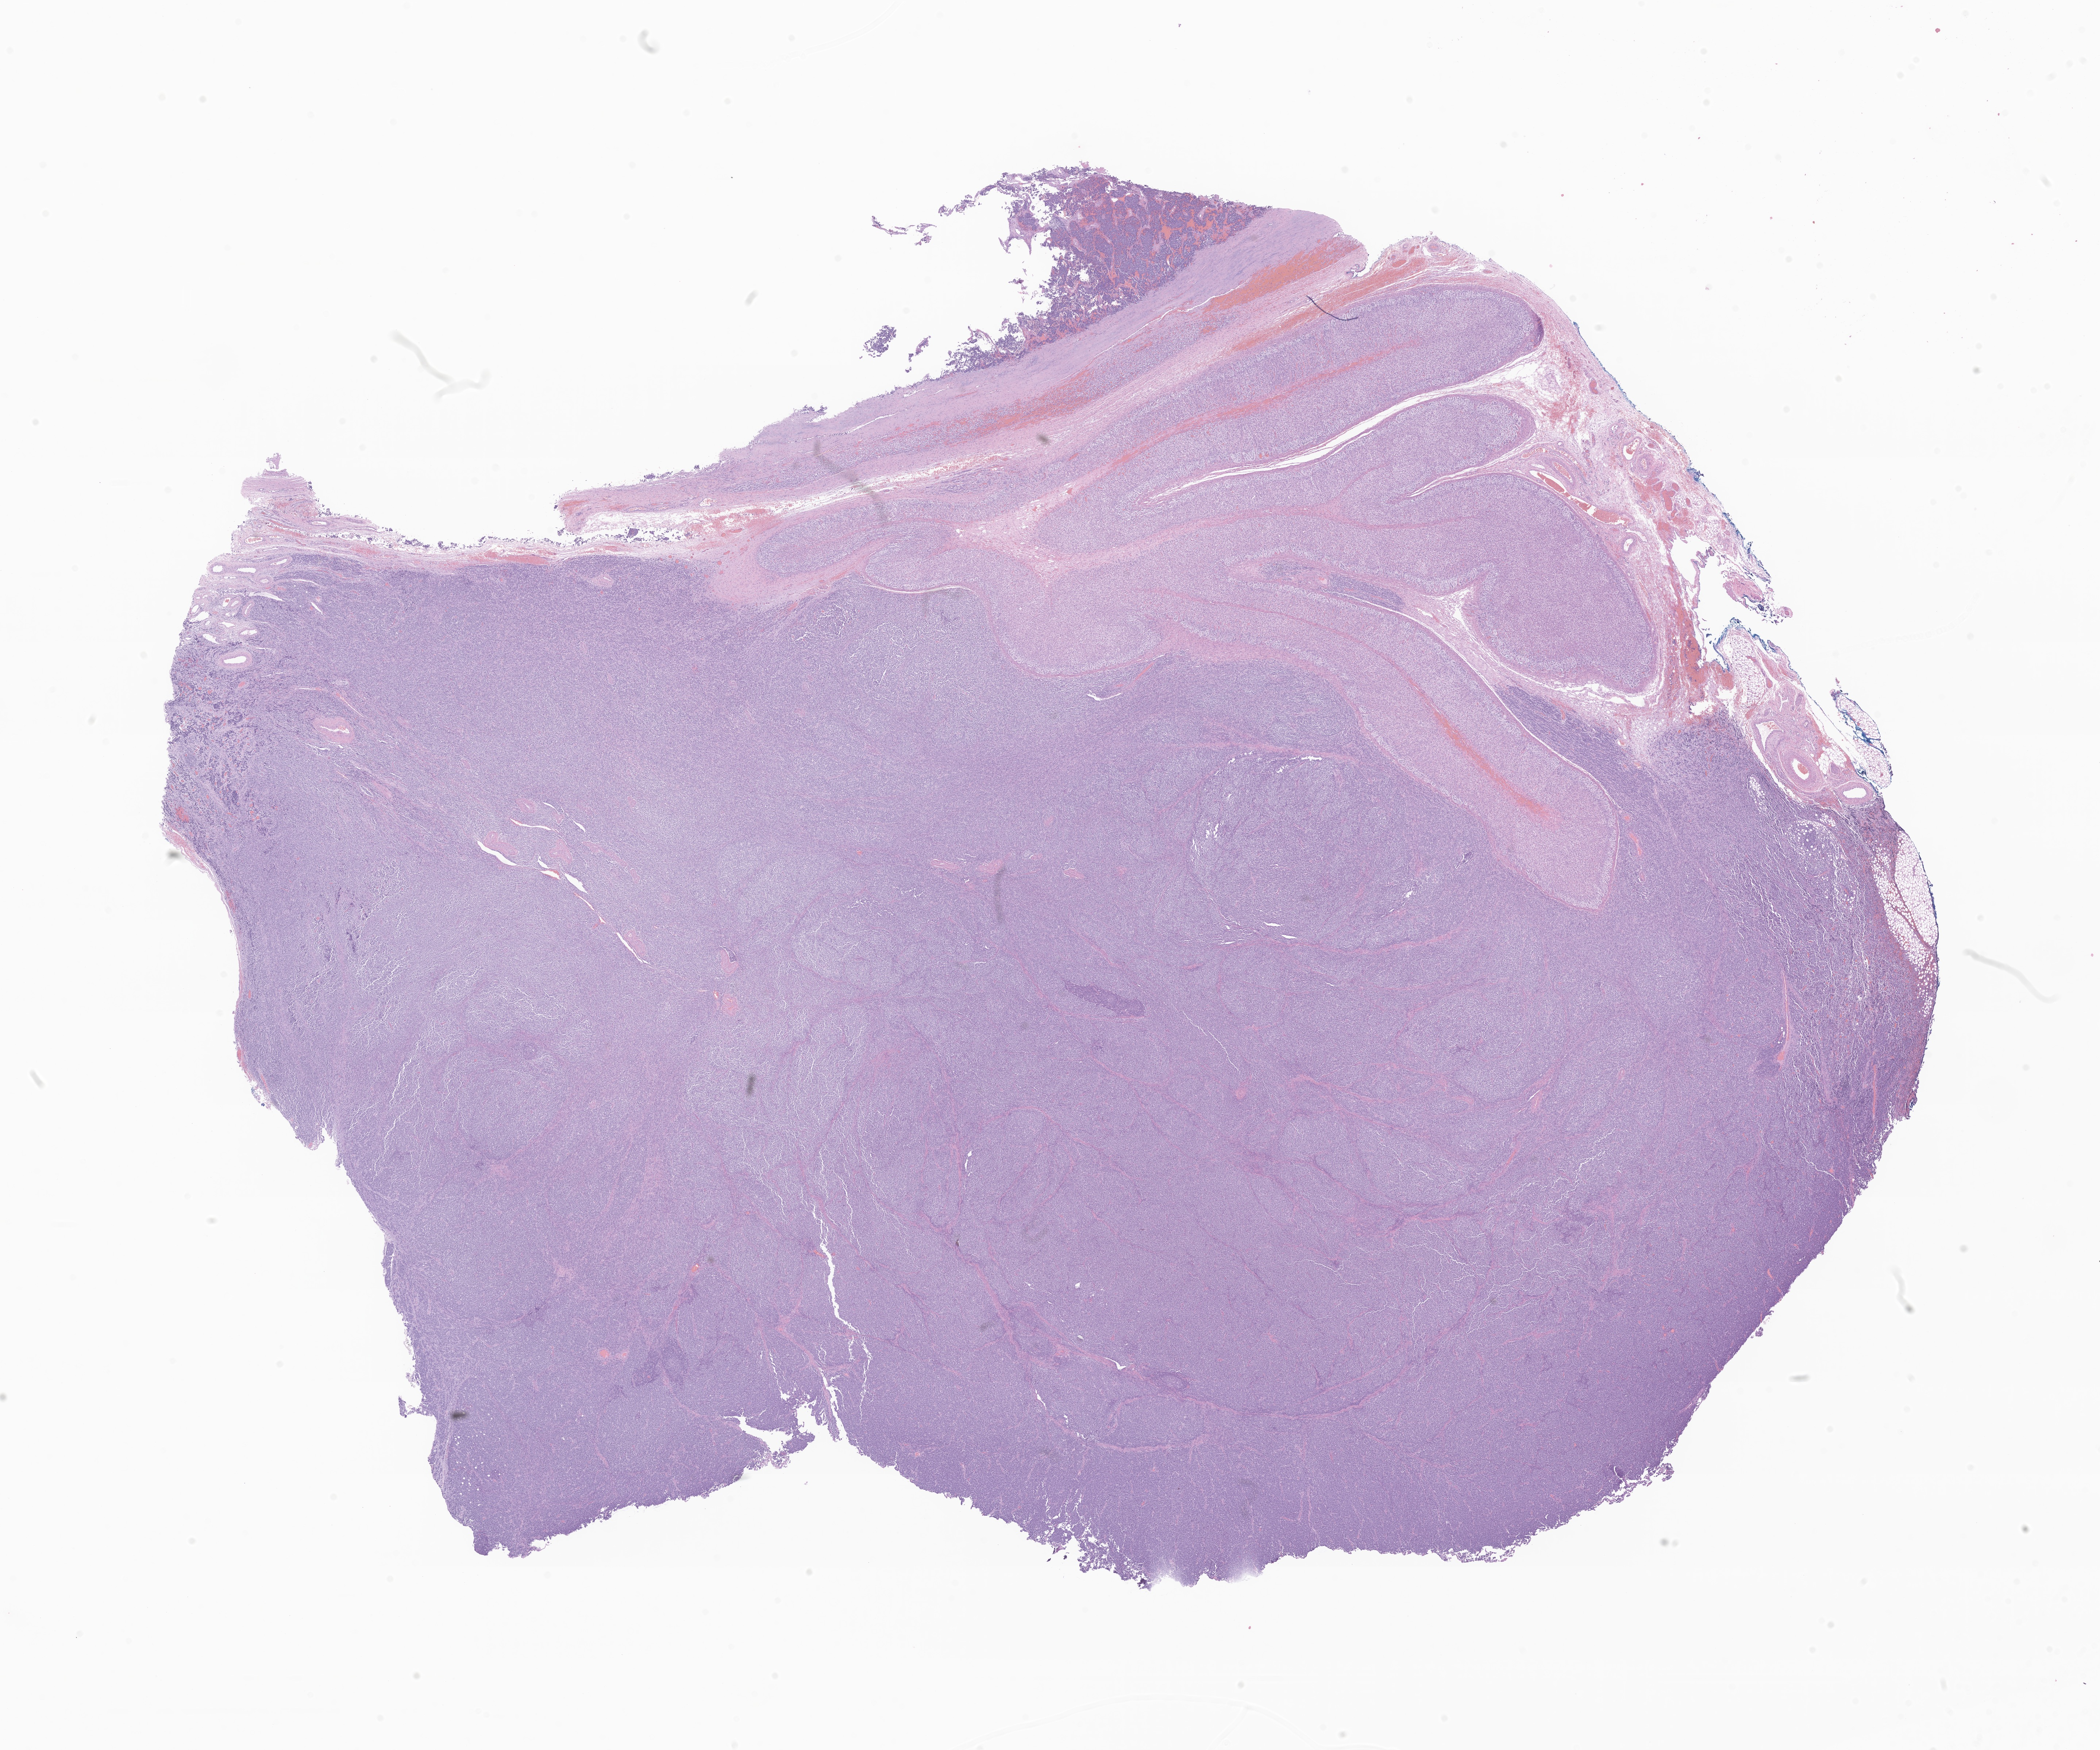
Whole-slide image, haematoxylin and eosin stain of tumor tissue from the retroperitoneum — whole scanned area (about 24.3 x 20.2 mm) shown as a low-resolution overview. Formalin-fixed paraffin-embedded section. Male patient, age 363 days.
Diagnosis: Neuroblastoma, NOS.